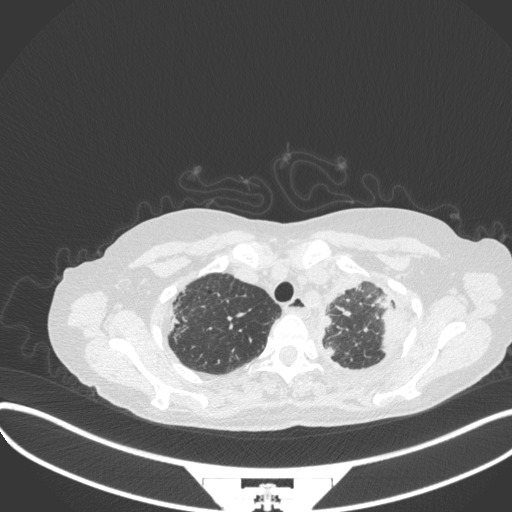
Chest CT, one axial slice; reconstruction kernel B31f; lung window (W 1500 / L -600 HU); 1 mm slice thickness; 512 × 512 image matrix, field of view 400 × 400 mm. Patient: female, 56 years. From the clinical record (not read from this slice): clinical TNM (as recorded): T1 N0 M0.
Outlined on this slice (bounding box drawn by a radiologist):
- lung tumour (recorded histology: adenocarcinoma): bounding box [x1, y1, x2, y2] px = [375, 293, 404, 351]